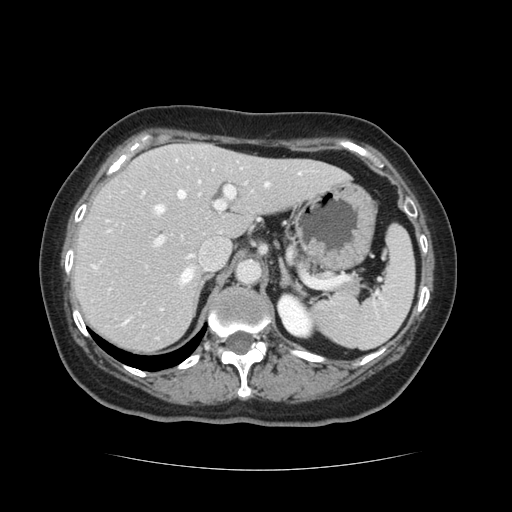
Contrast-enhanced abdominal CT, one axial slice; slice 84 of 128 in the series (ordered by position); intravenous contrast given; soft-tissue window (W 400 / L 40 HU); 512 × 512 image matrix, field of view 366 × 366 mm. Female patient, age 67 years. From the clinical record (not read from this slice): diagnosis: colorectal cancer liver metastases, imaged before liver resection; multiple liver metastases: yes; largest metastasis: 3 cm; disease in both lobes: yes.
Structures marked on this image (outlined manually by an expert reader):
- hepatic veins: bounding box (x1, y1, x2, y2) in pixels: (128, 173, 301, 321)
- liver: (74, 145, 345, 353)
- planned liver remnant (the part of the liver to remain after resection): (74, 157, 345, 352)
- portal vein (with intrahepatic branches): (157, 168, 247, 244)